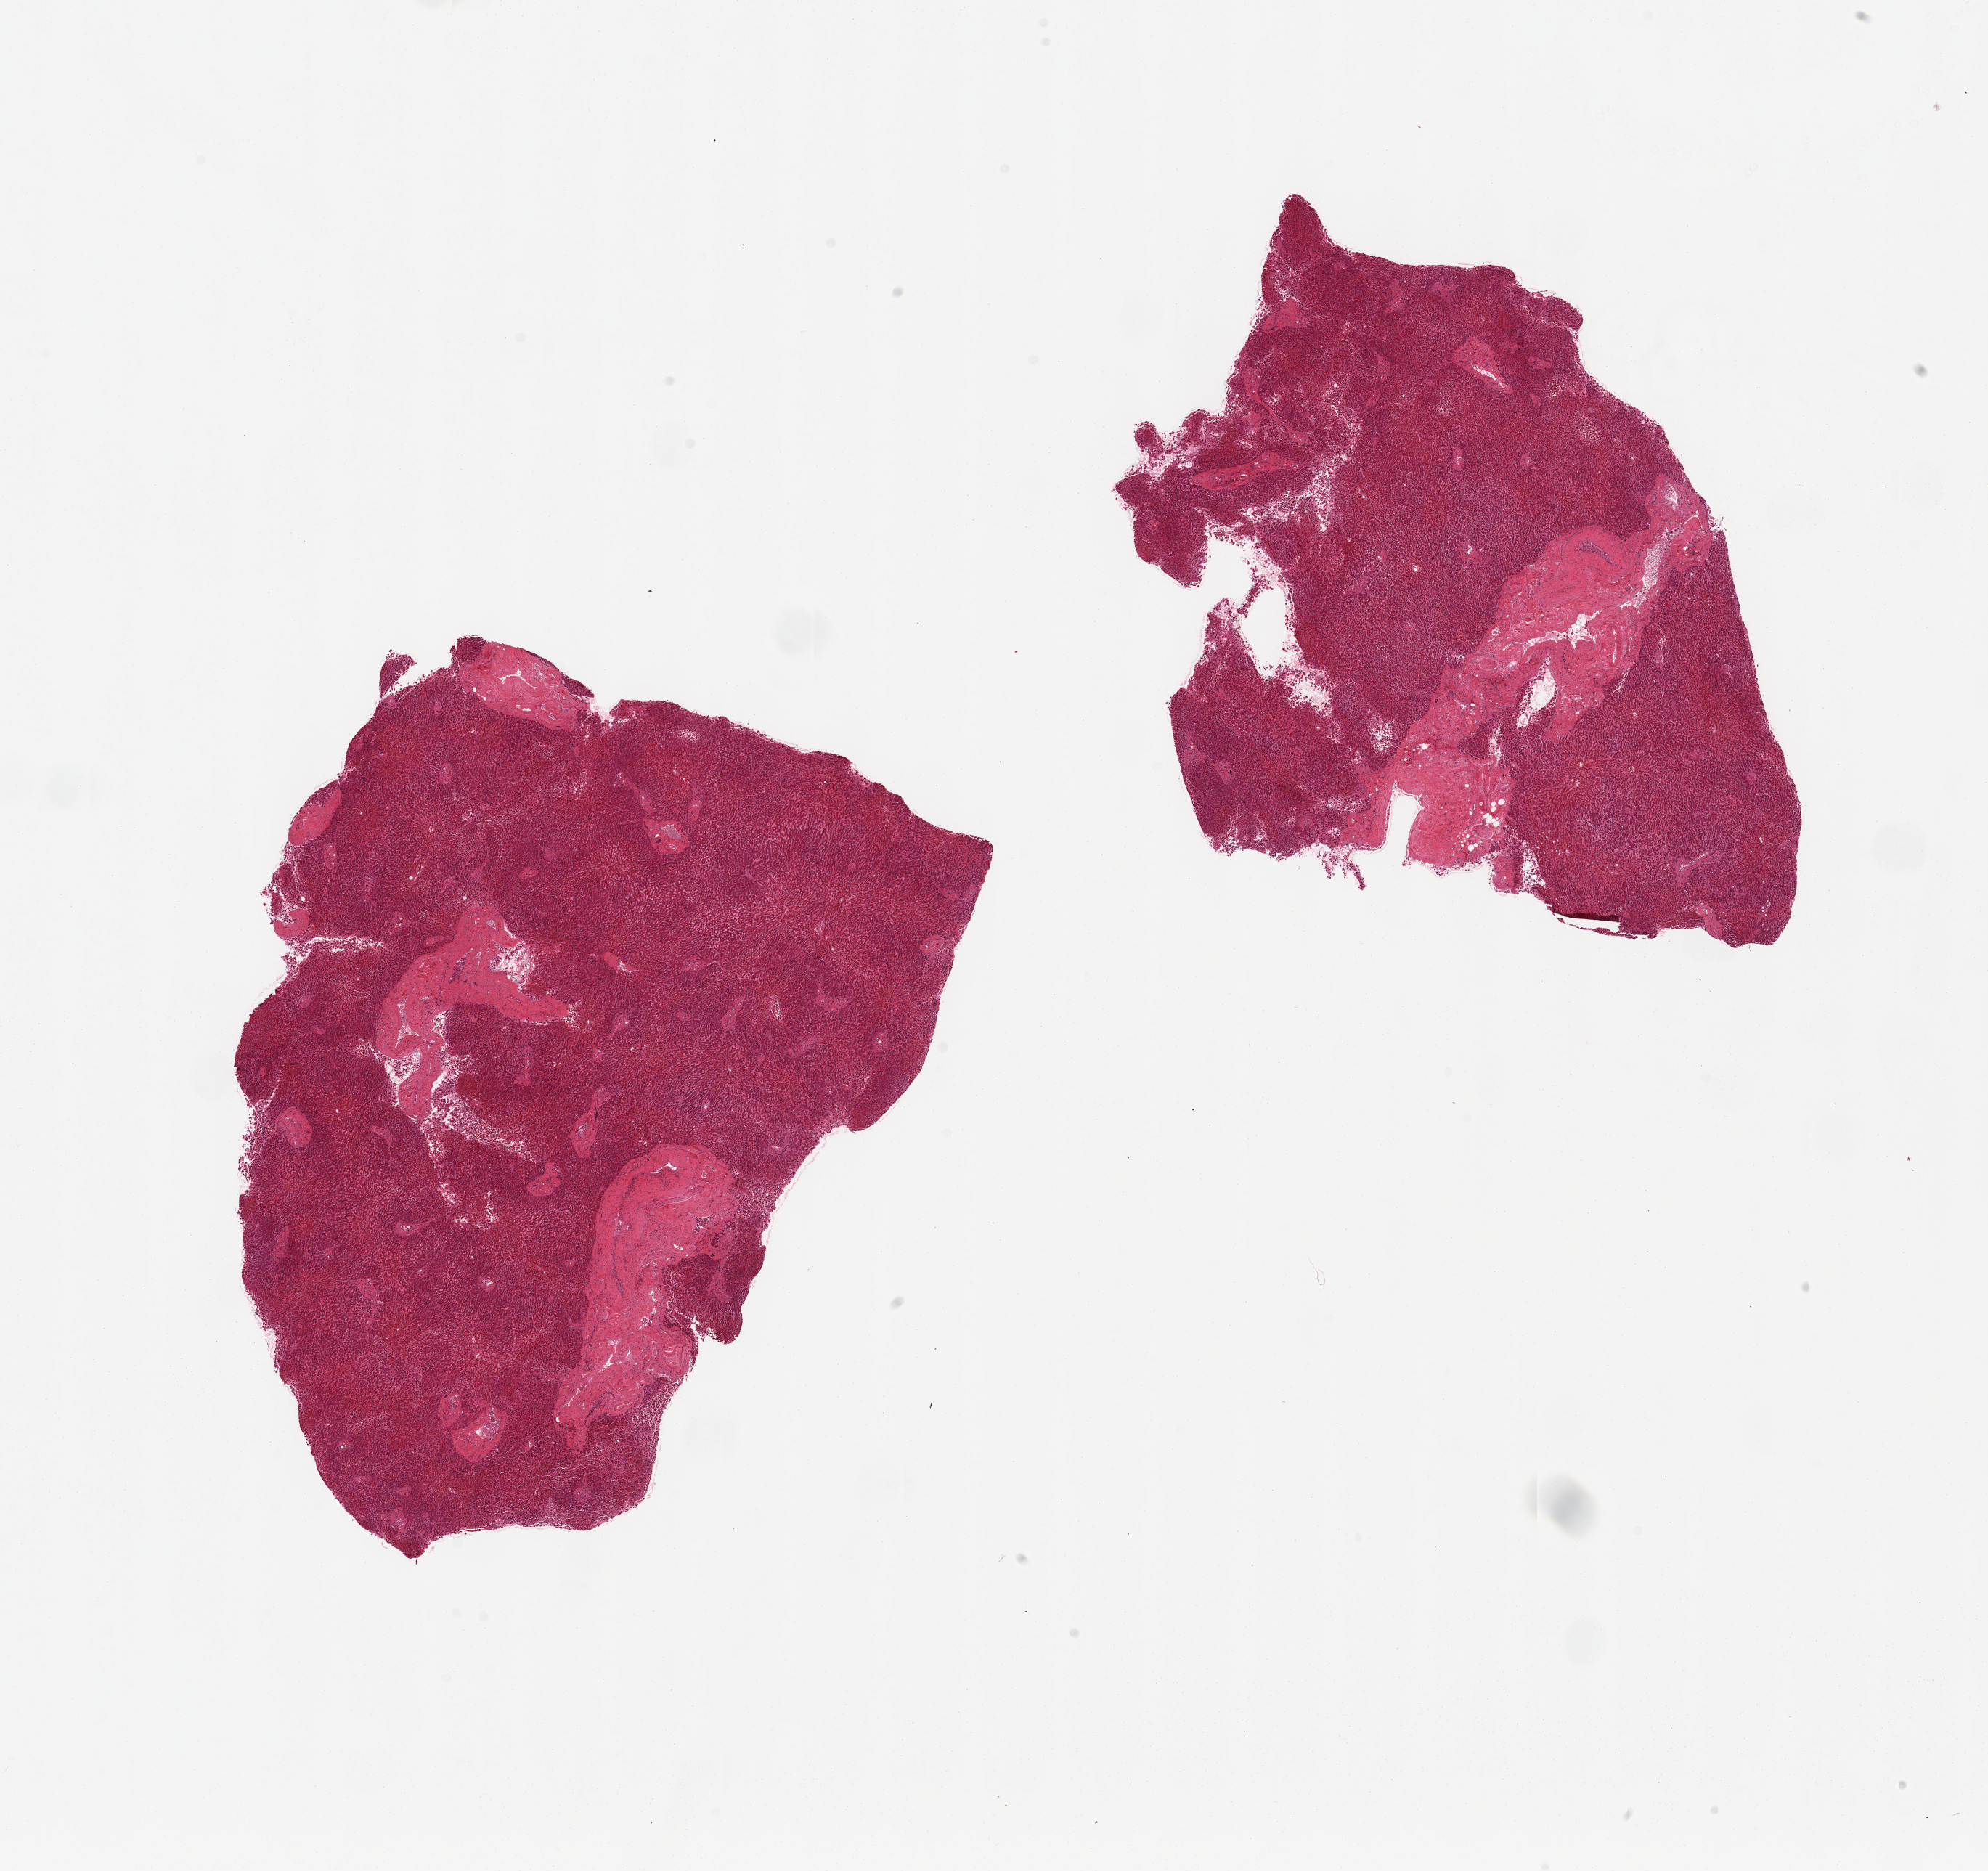
Whole-slide image, haematoxylin and eosin stain — a low-resolution overview of the entire scanned area, about 21.7 x 20.4 mm, PAXgene-fixed, paraffin-embedded tissue, target tissue: liver, donor tissue sample. Donor sex: male.
* reviewer comment on this tissue sample: 2 pieces; 10-20% of each is large vessels/nerve/fibrous tissue